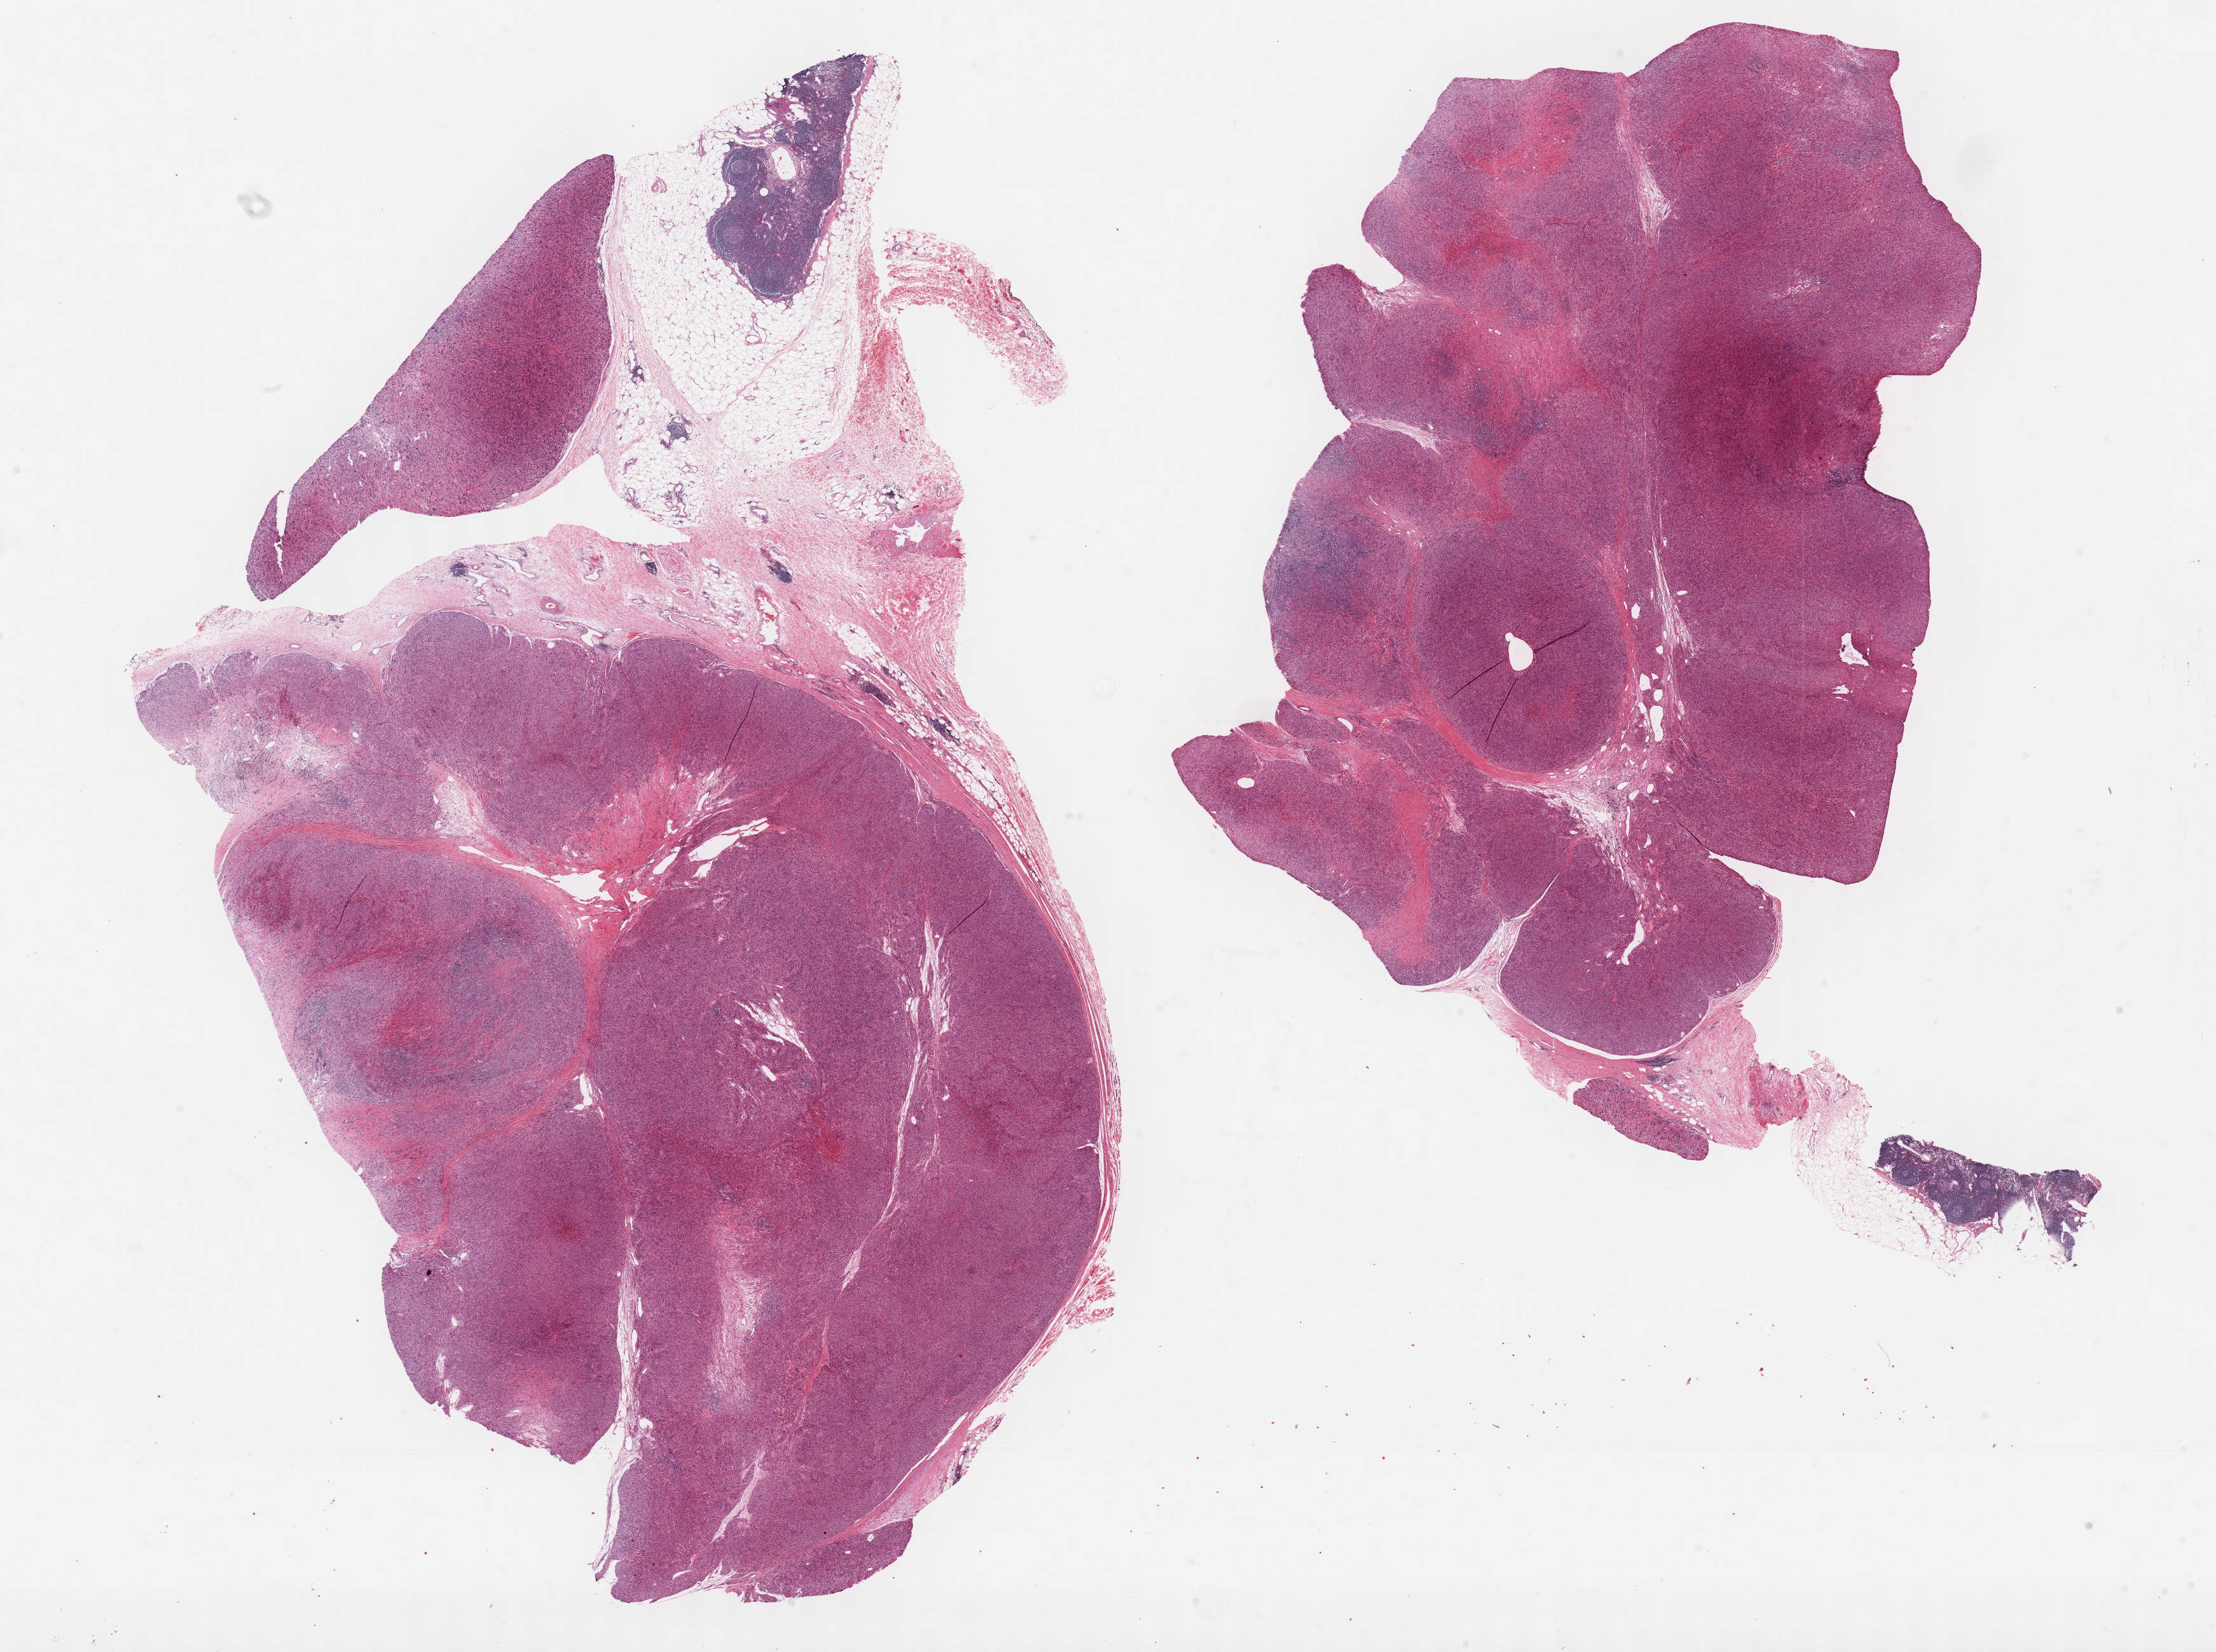
Digitized H&E-stained tissue section (whole slide) — shown as a low-resolution overview of the whole scanned area (about 28.2 x 21.0 mm, acquisition: 40x scan), FFPE section, primary tumour sample from the retroperitoneum and peritoneum. Male patient; age at initial diagnosis 70 years.
Diagnosis: Leiomyosarcoma, NOS (retroperitoneum).